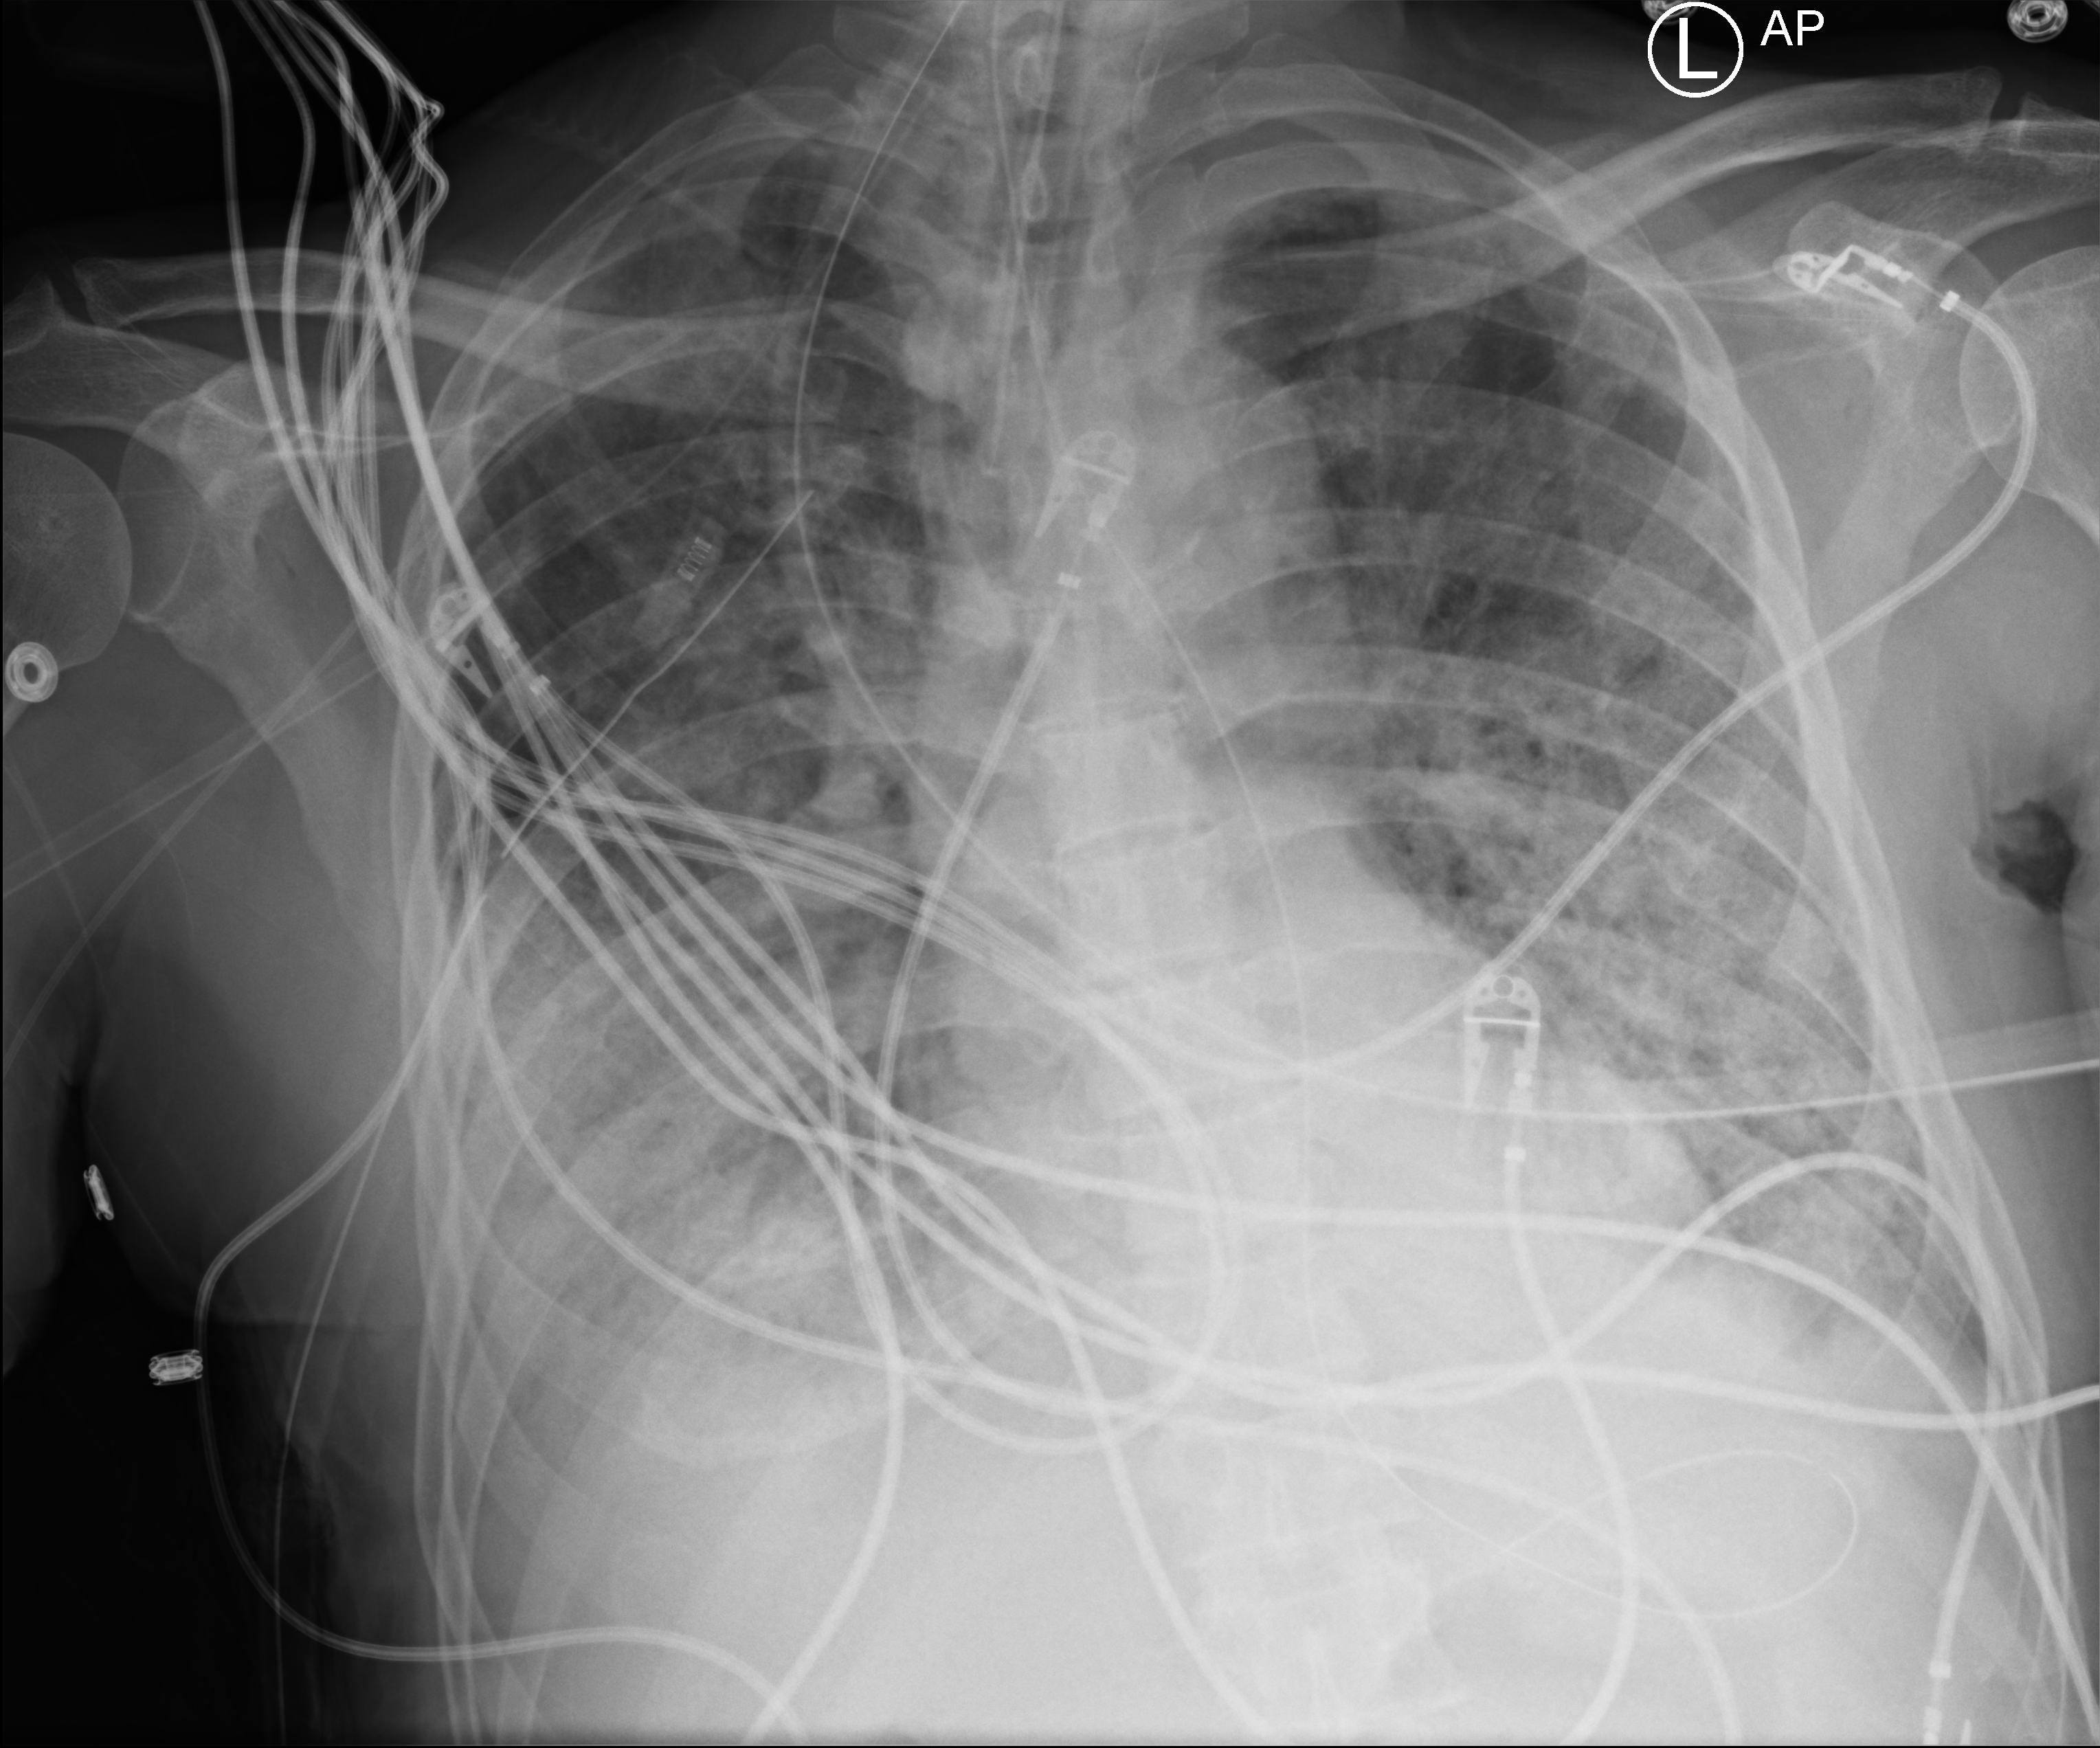
Portable chest radiograph, anteroposterior (AP) projection. Male patient hospitalised with COVID-19, age 60–74 years.
Hospital-stay facts (about this admission, not read from this image; timing relative to this image not recorded): admitted to intensive care during this hospital stay: yes; COPD (admission record): no.